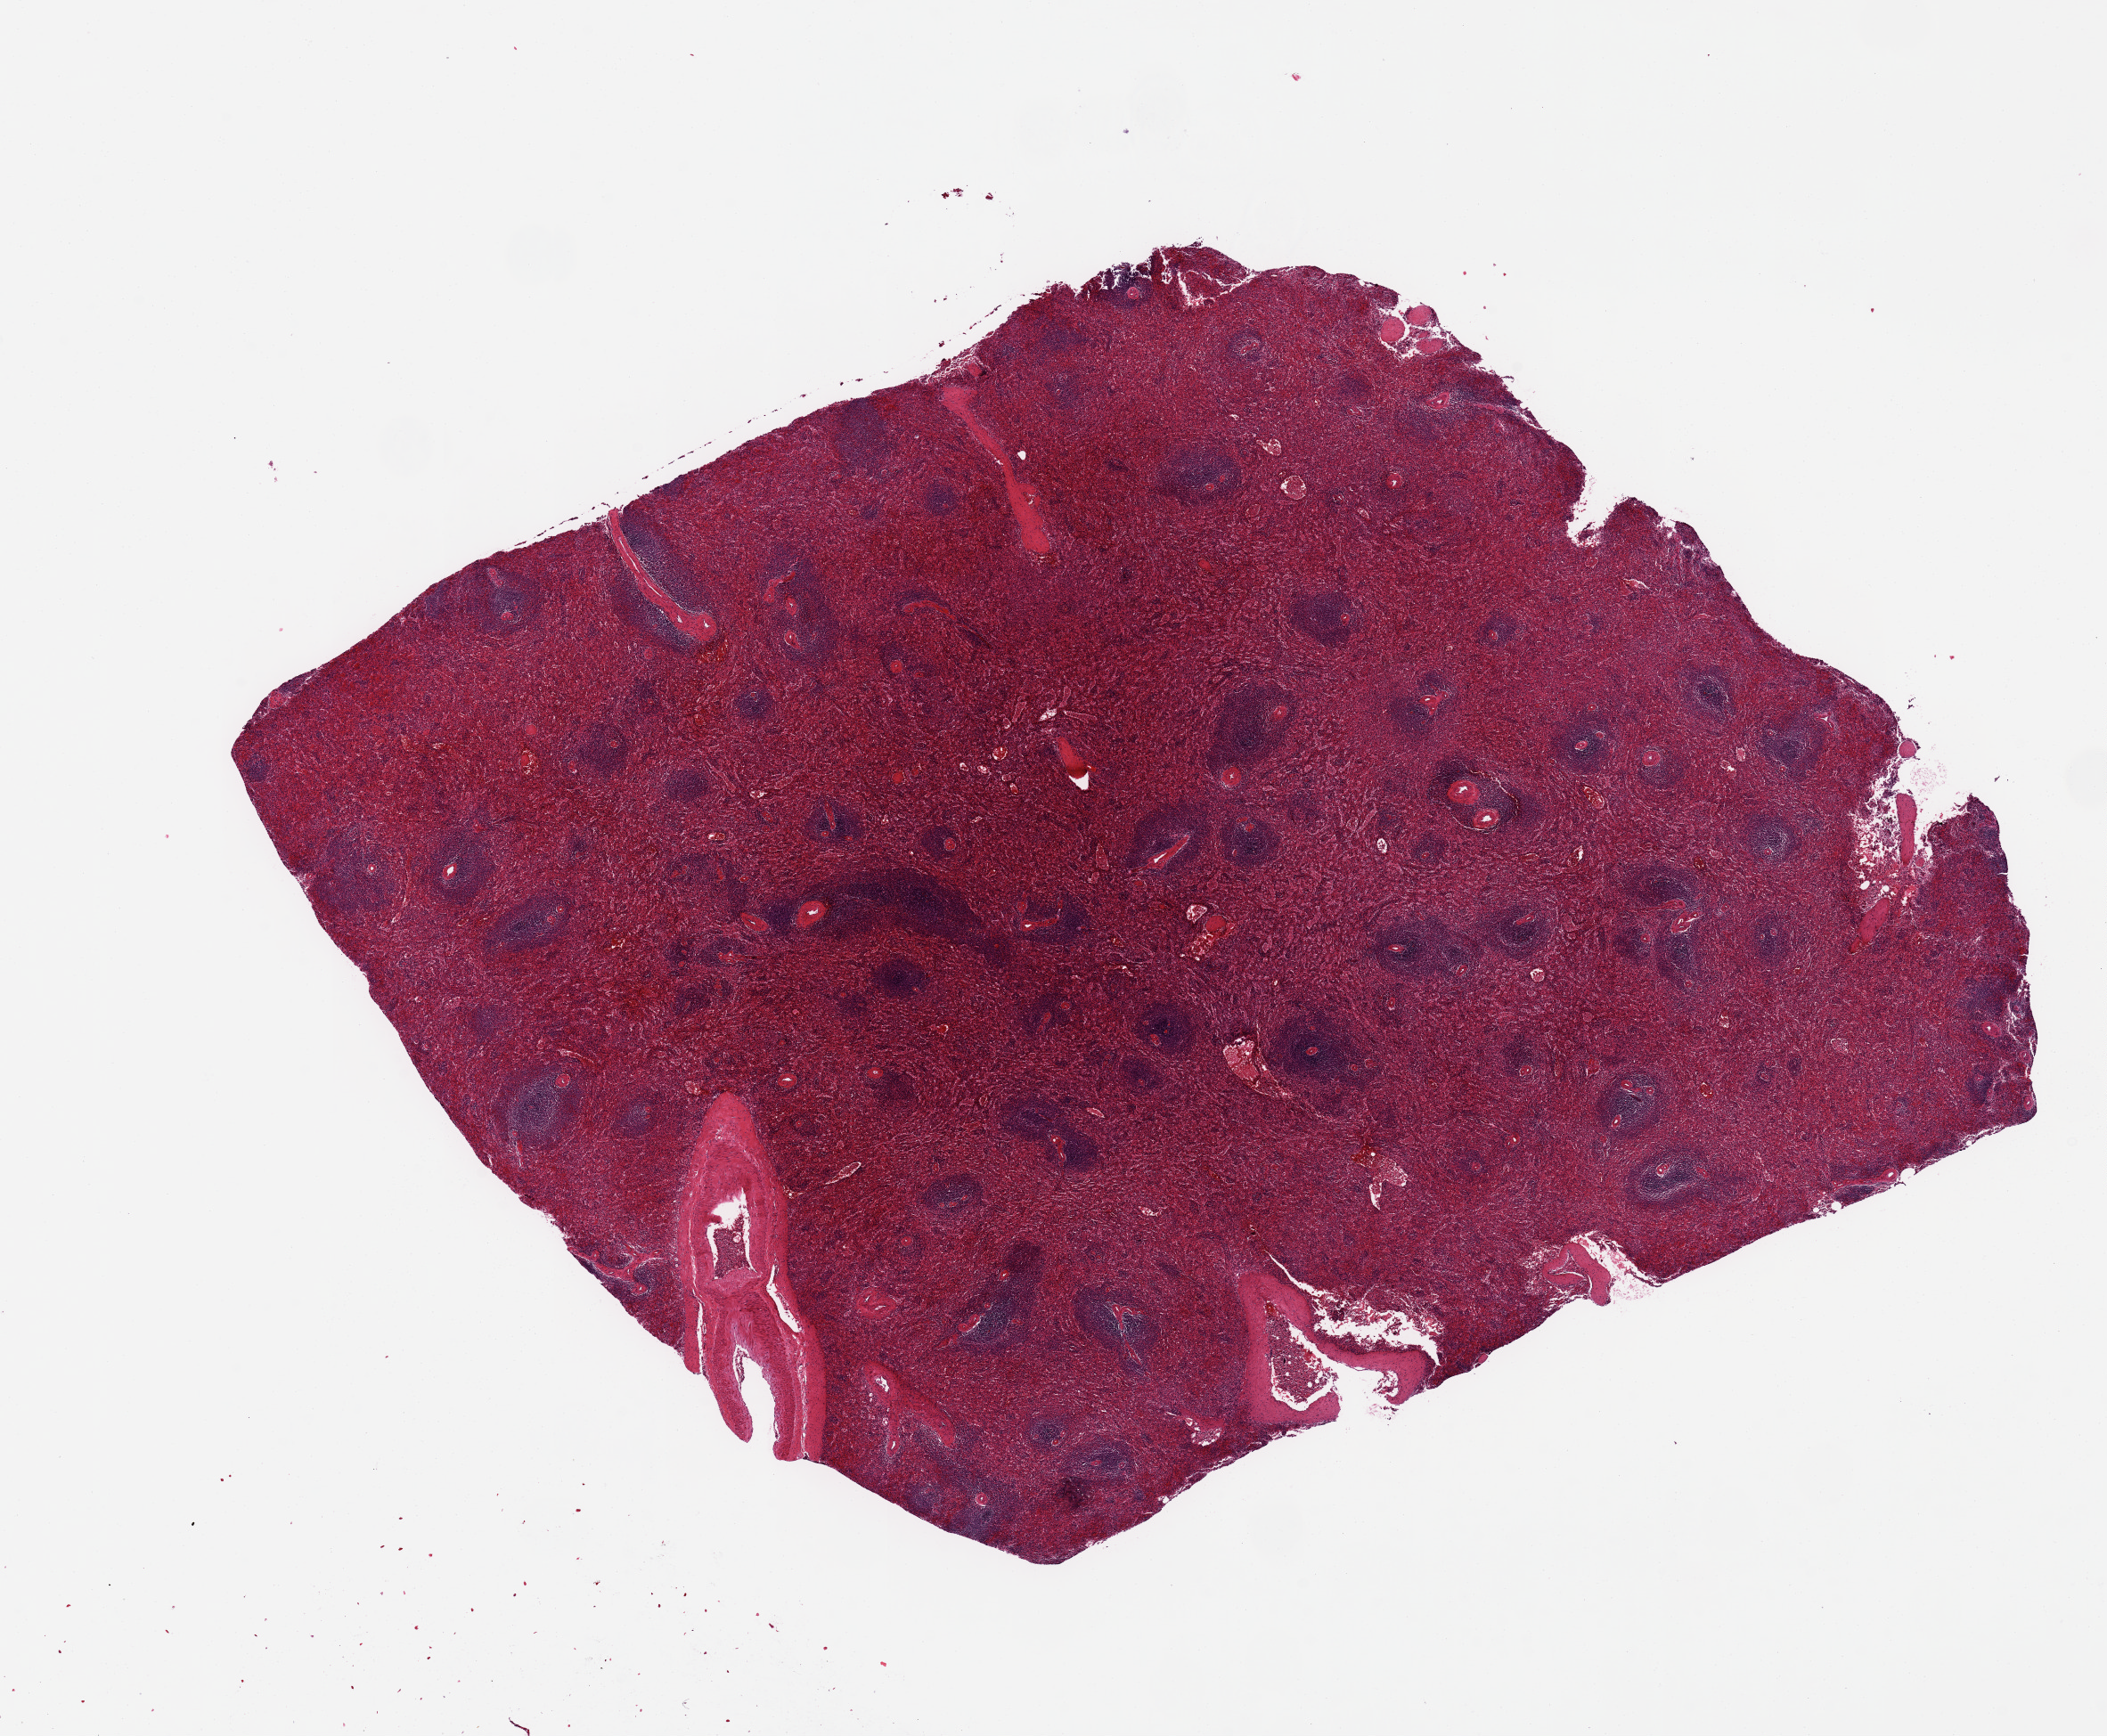
Hematoxylin and eosin (H&E) whole-slide image, whole scanned area (about 18.7 x 15.4 mm) shown as a low-resolution overview; PAXgene-fixed, paraffin-embedded tissue; sampled site (target tissue): spleen; tissue donor sample. Donor sex: male.
Review note (as recorded): 12x10 mm.